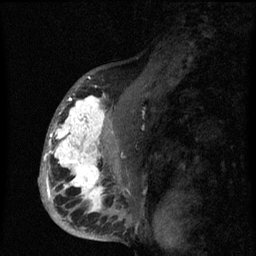
Breast MRI (dynamic contrast-enhanced), one sagittal slice. Slice 39 of 60 in the series (ordered by position). Dynamic contrast-enhanced series, image 2 of 3 at this slice position (ordered by acquisition). 1.5 T. TE 4.2 ms, TR 8 ms. 2 mm slice thickness. 256 × 256 image matrix, field of view 190 × 190 mm. Patient: female, 50 years.
Structures marked on this image (semi-automatically segmented with operator editing):
- analysis volume of interest (the breast-tissue region the enhancement analysis was run in; not a lesion): box from (x=43, y=90) to (x=142, y=216) px
- tumour enhancement mask (voxels above the 70 % enhancement threshold inside the analysis volume of interest): (x=43, y=95)–(x=127, y=211)